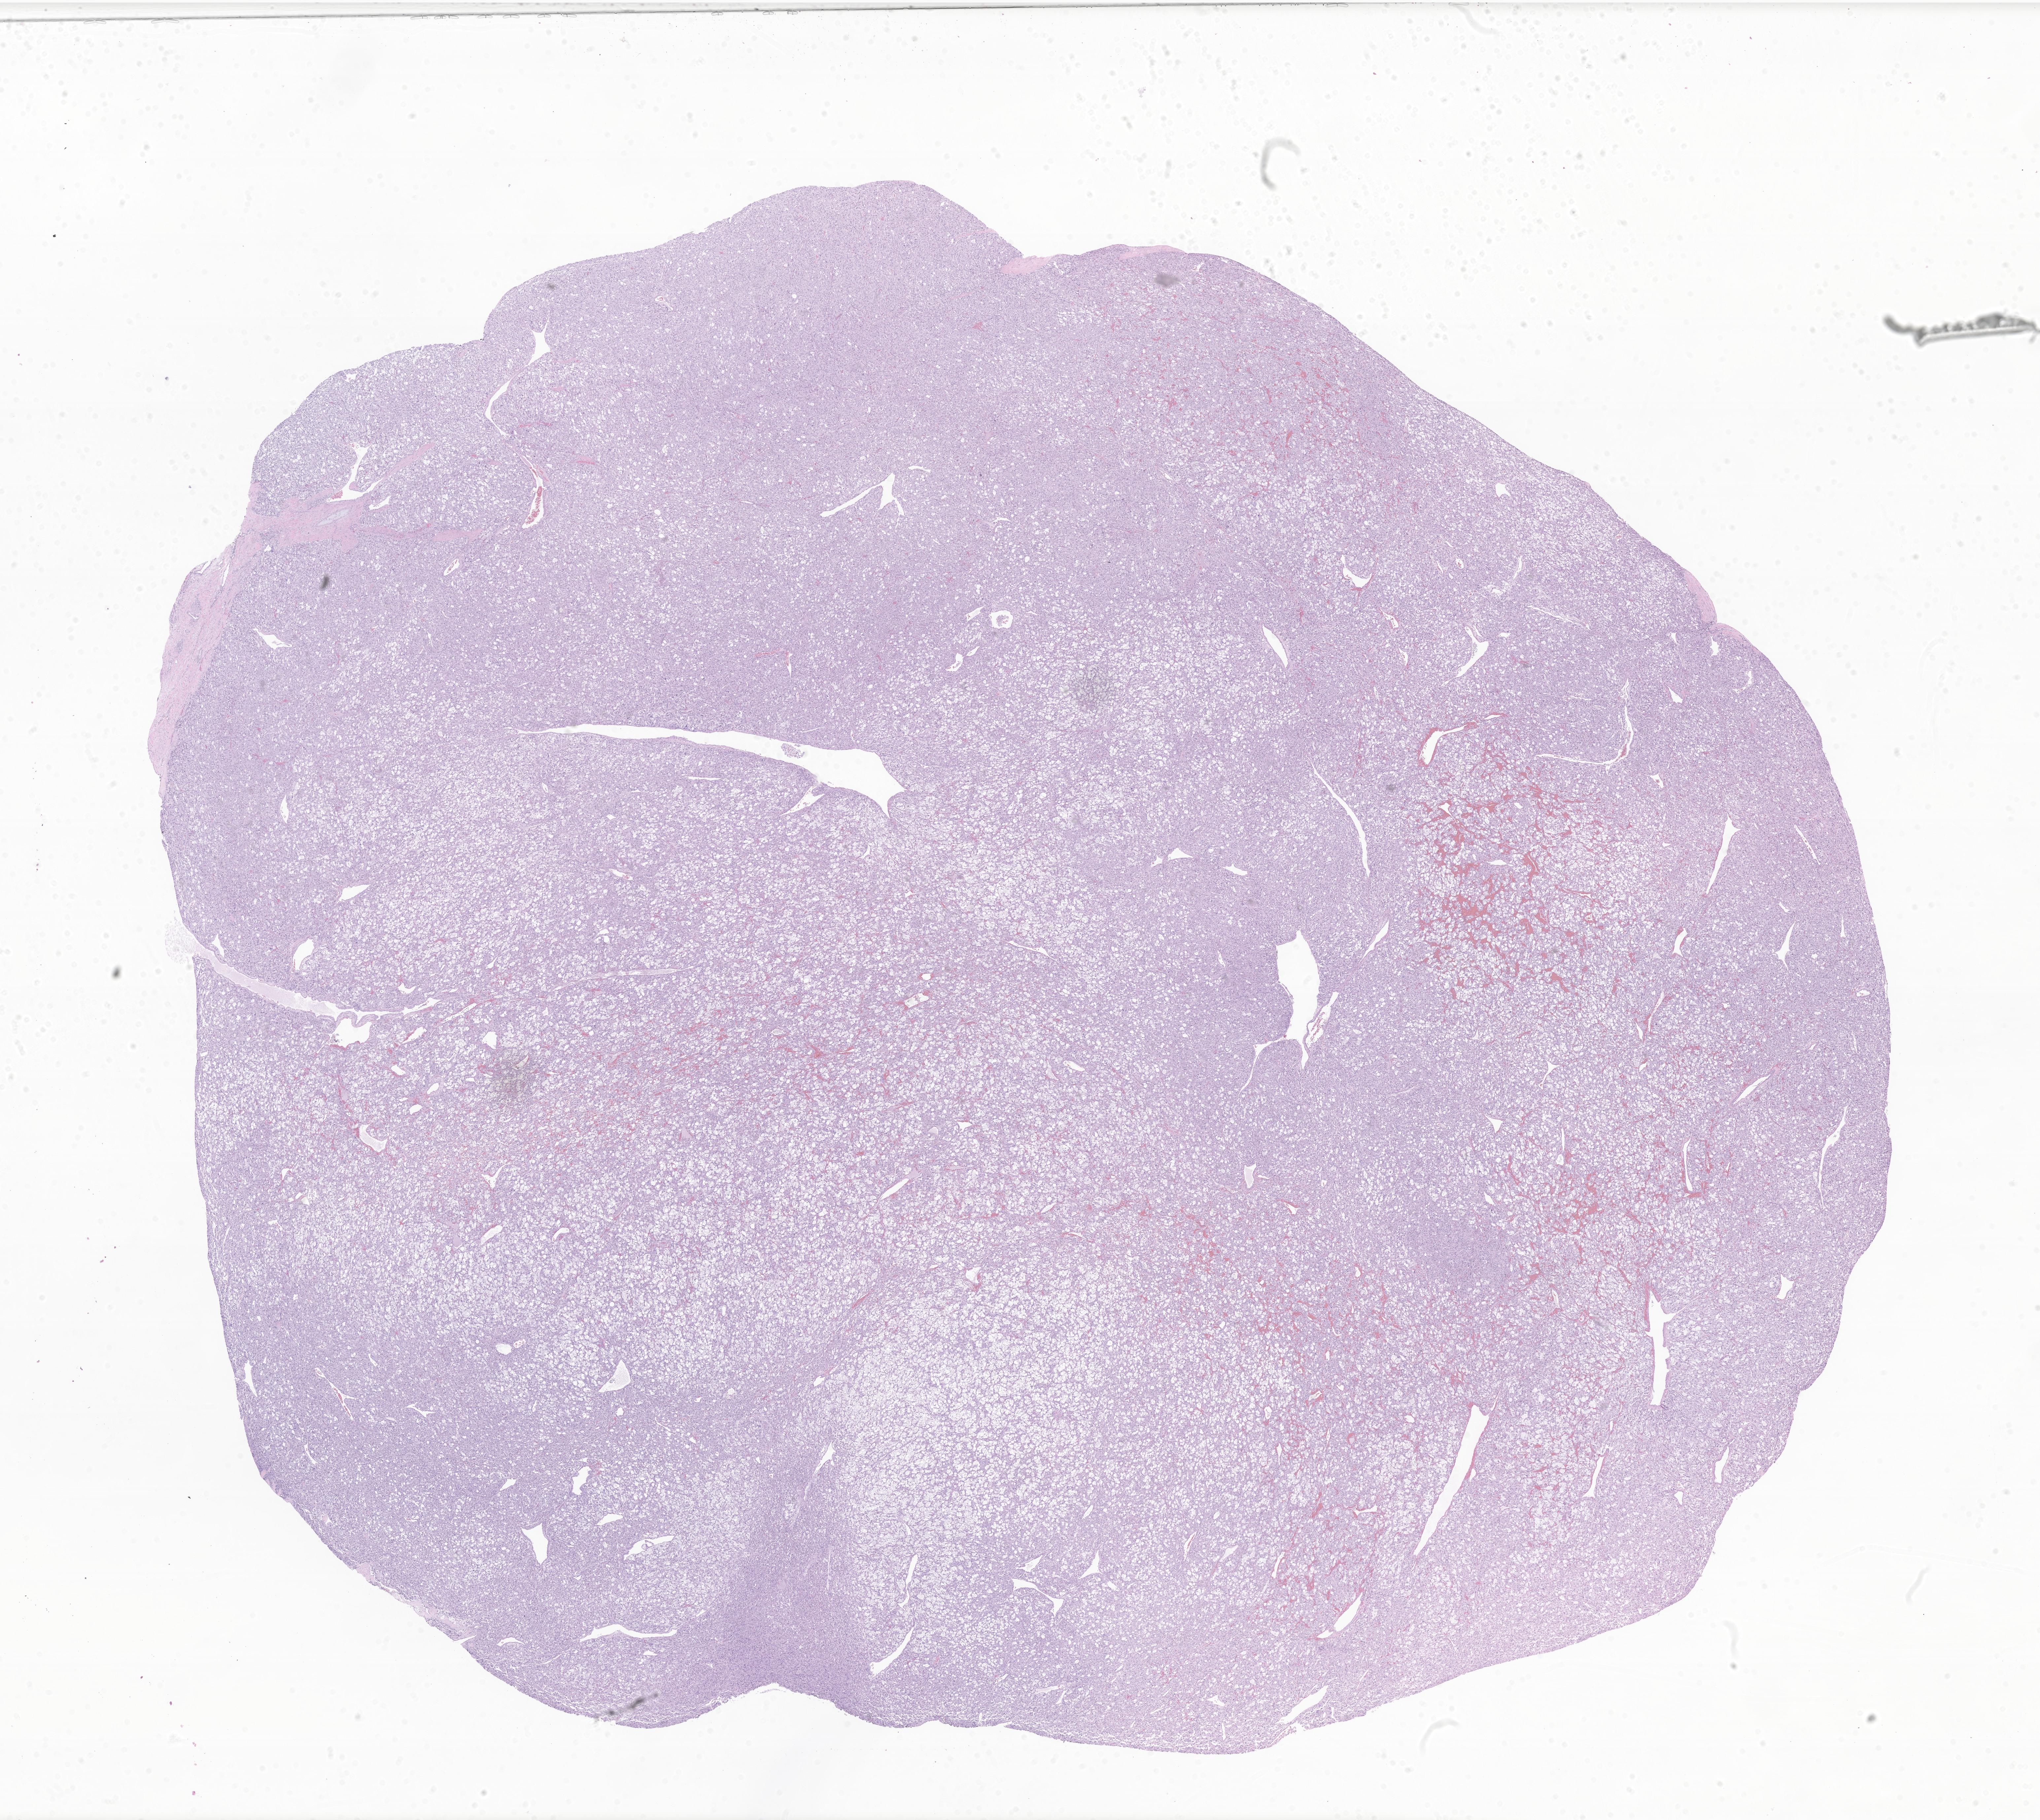
Hematoxylin and eosin (H&E) whole-slide image of tumor tissue from the adrenal gland — whole scanned area (about 26.0 x 23.2 mm) shown as a low-resolution overview. Formalin-fixed, paraffin-embedded (FFPE) tissue. Patient female; age 205 months (17 years 1 month).
Diagnosis: Paraganglioma, NOS.